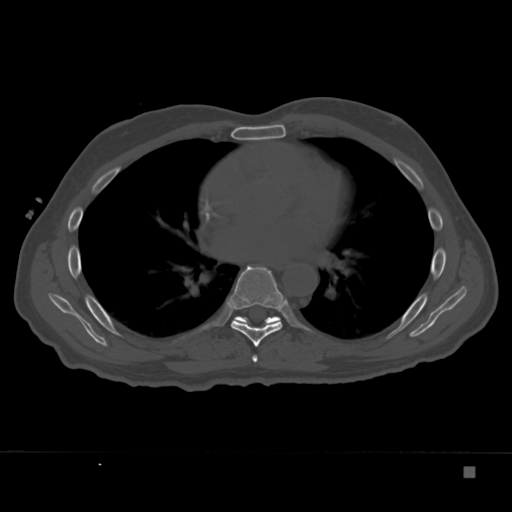
CT including the spine, one axial slice. Slice 220 of 332 in the series (ordered by position). Reconstruction kernel Br40s. Bone window (W 1800 / L 400 HU). 1.5 mm slice thickness. 512 × 512 image matrix. Patient: male, 72 years. From the clinical record (not read from this slice): primary cancer: skeletal.
Outlined on this slice (semi-automatically segmented with operator editing):
- T6 vertebra: box from (x=252, y=355) to (x=258, y=363) px
- T7 vertebra: (x=230, y=265)–(x=285, y=347)
- T8 vertebra: (x=233, y=316)–(x=281, y=325)